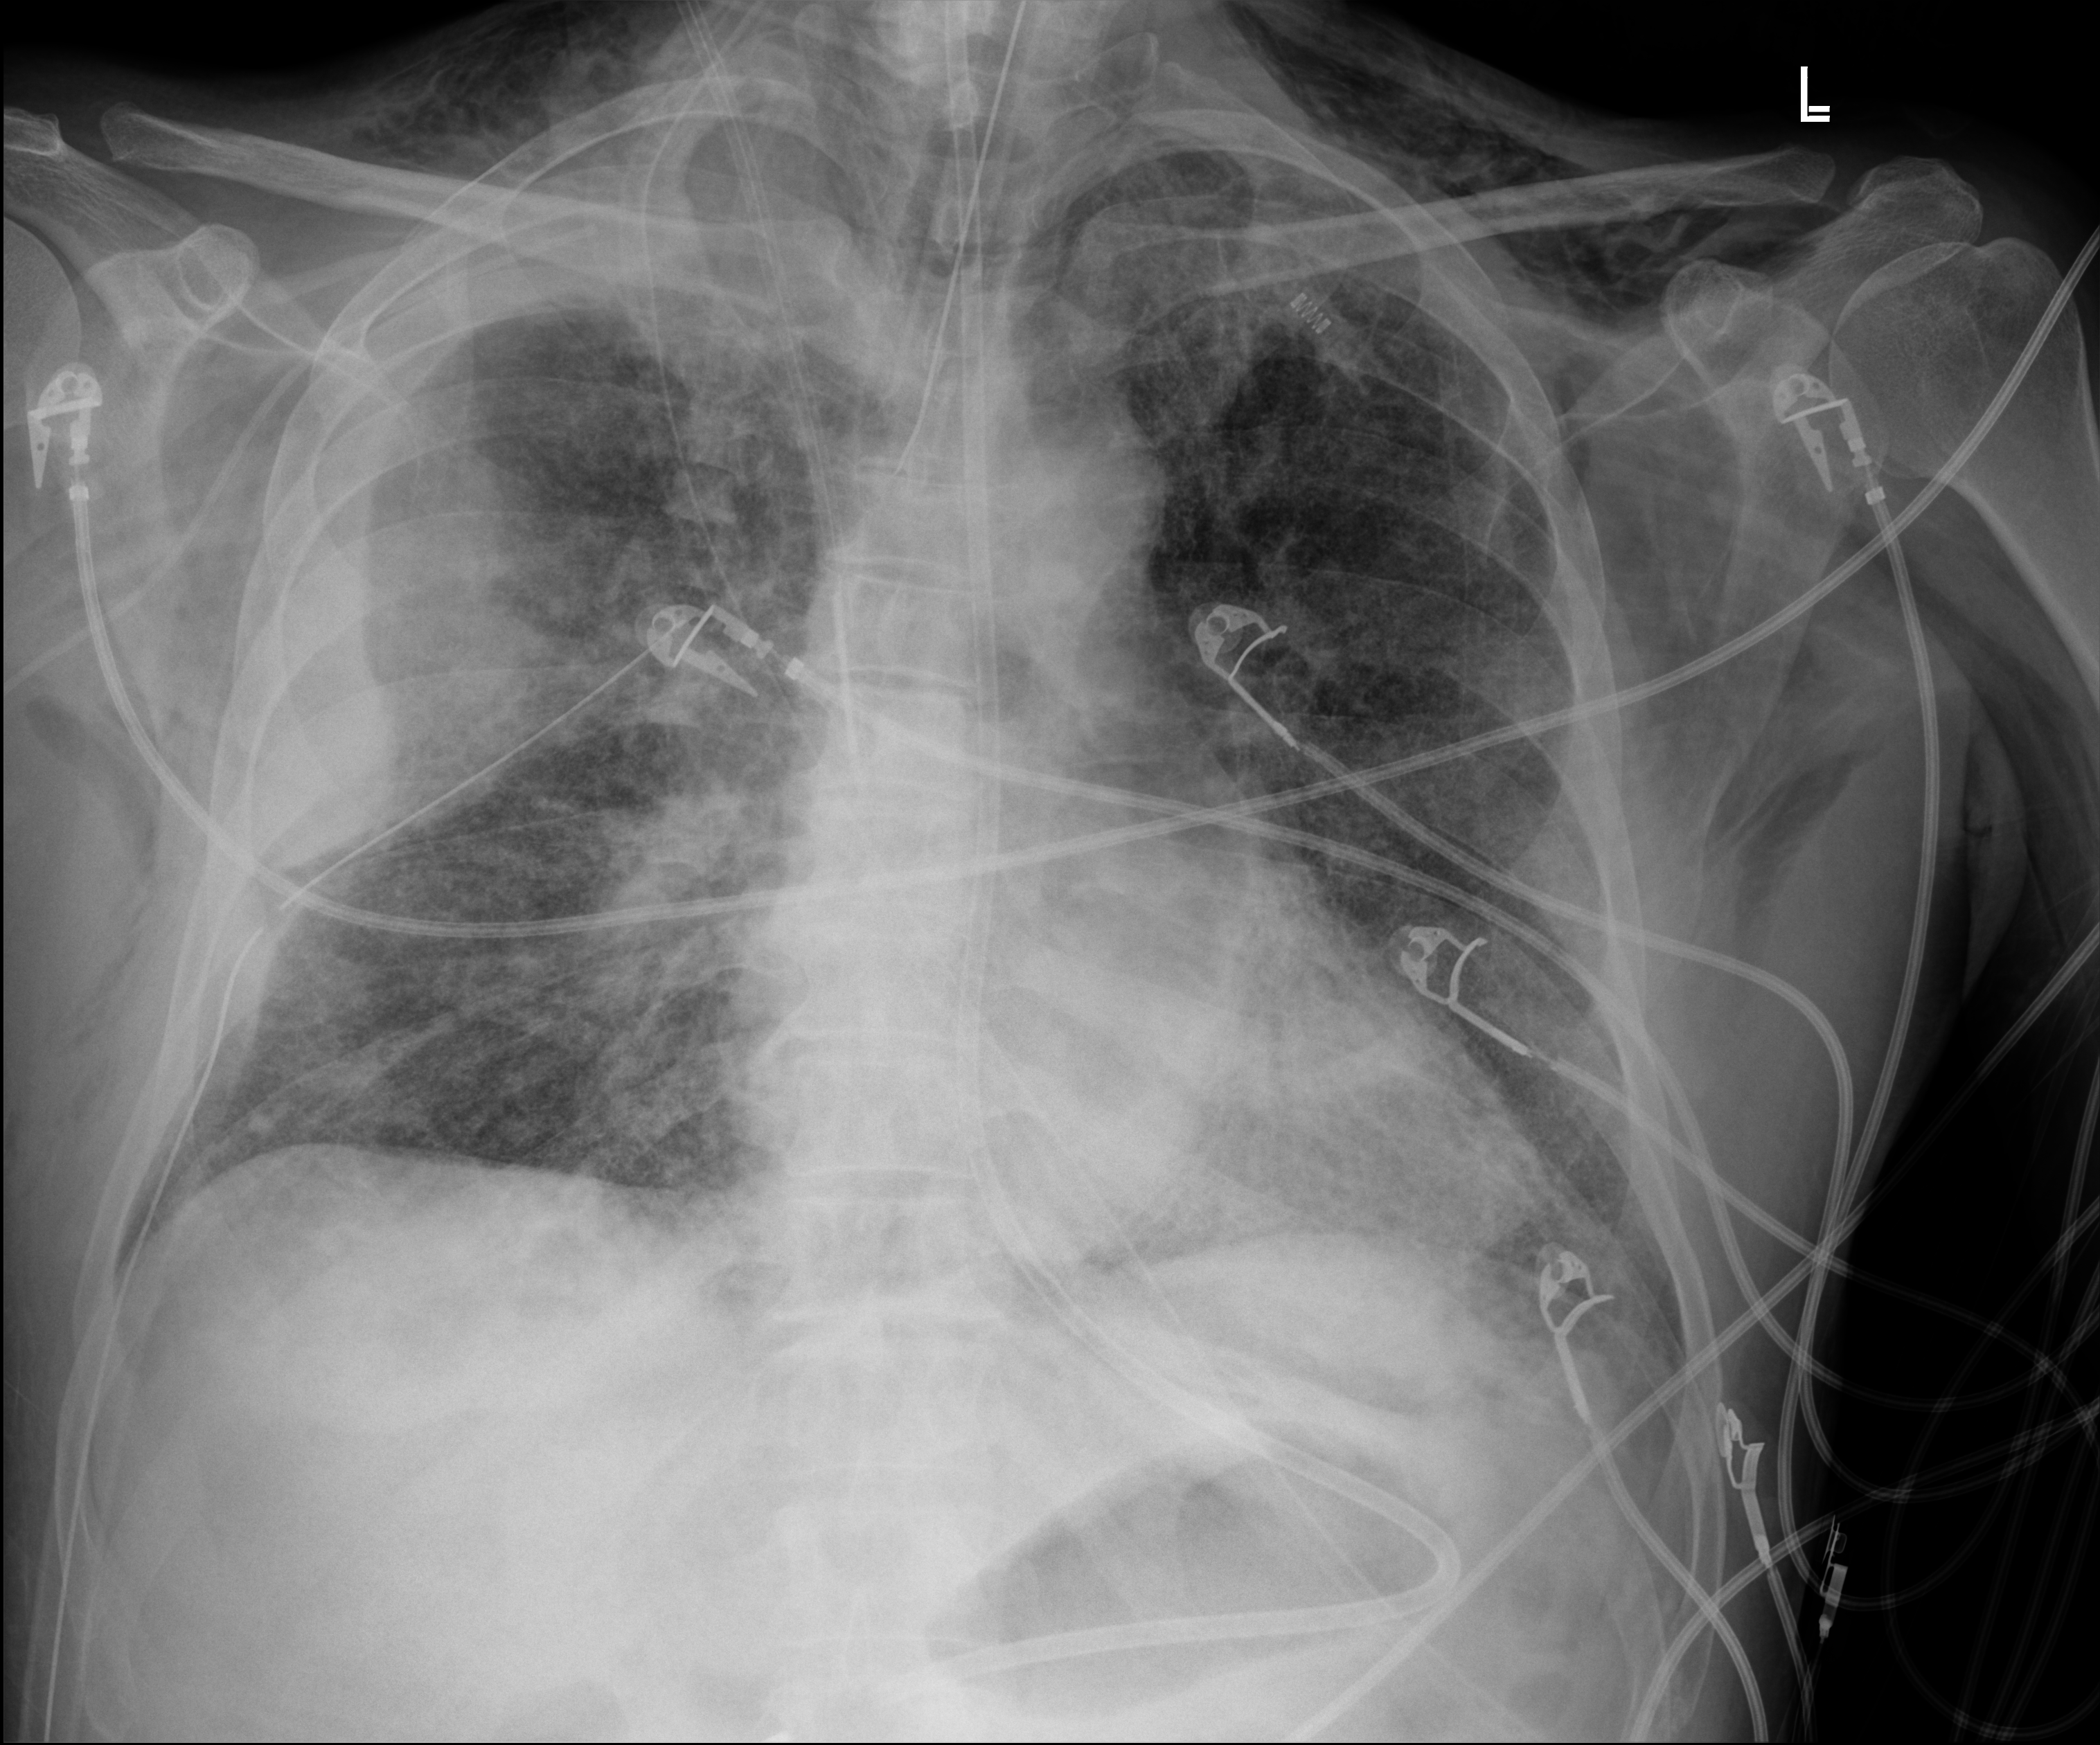
Bedside chest radiograph (digital radiography). Patient hospitalised with COVID-19; male, aged 18–59 years.
From the hospital-stay record, not from the radiograph (when in the stay this image was taken is not recorded):
- admitted to intensive care during this hospital stay: yes
- mechanically ventilated during this hospital stay: yes
- chronic kidney disease (admission record): no